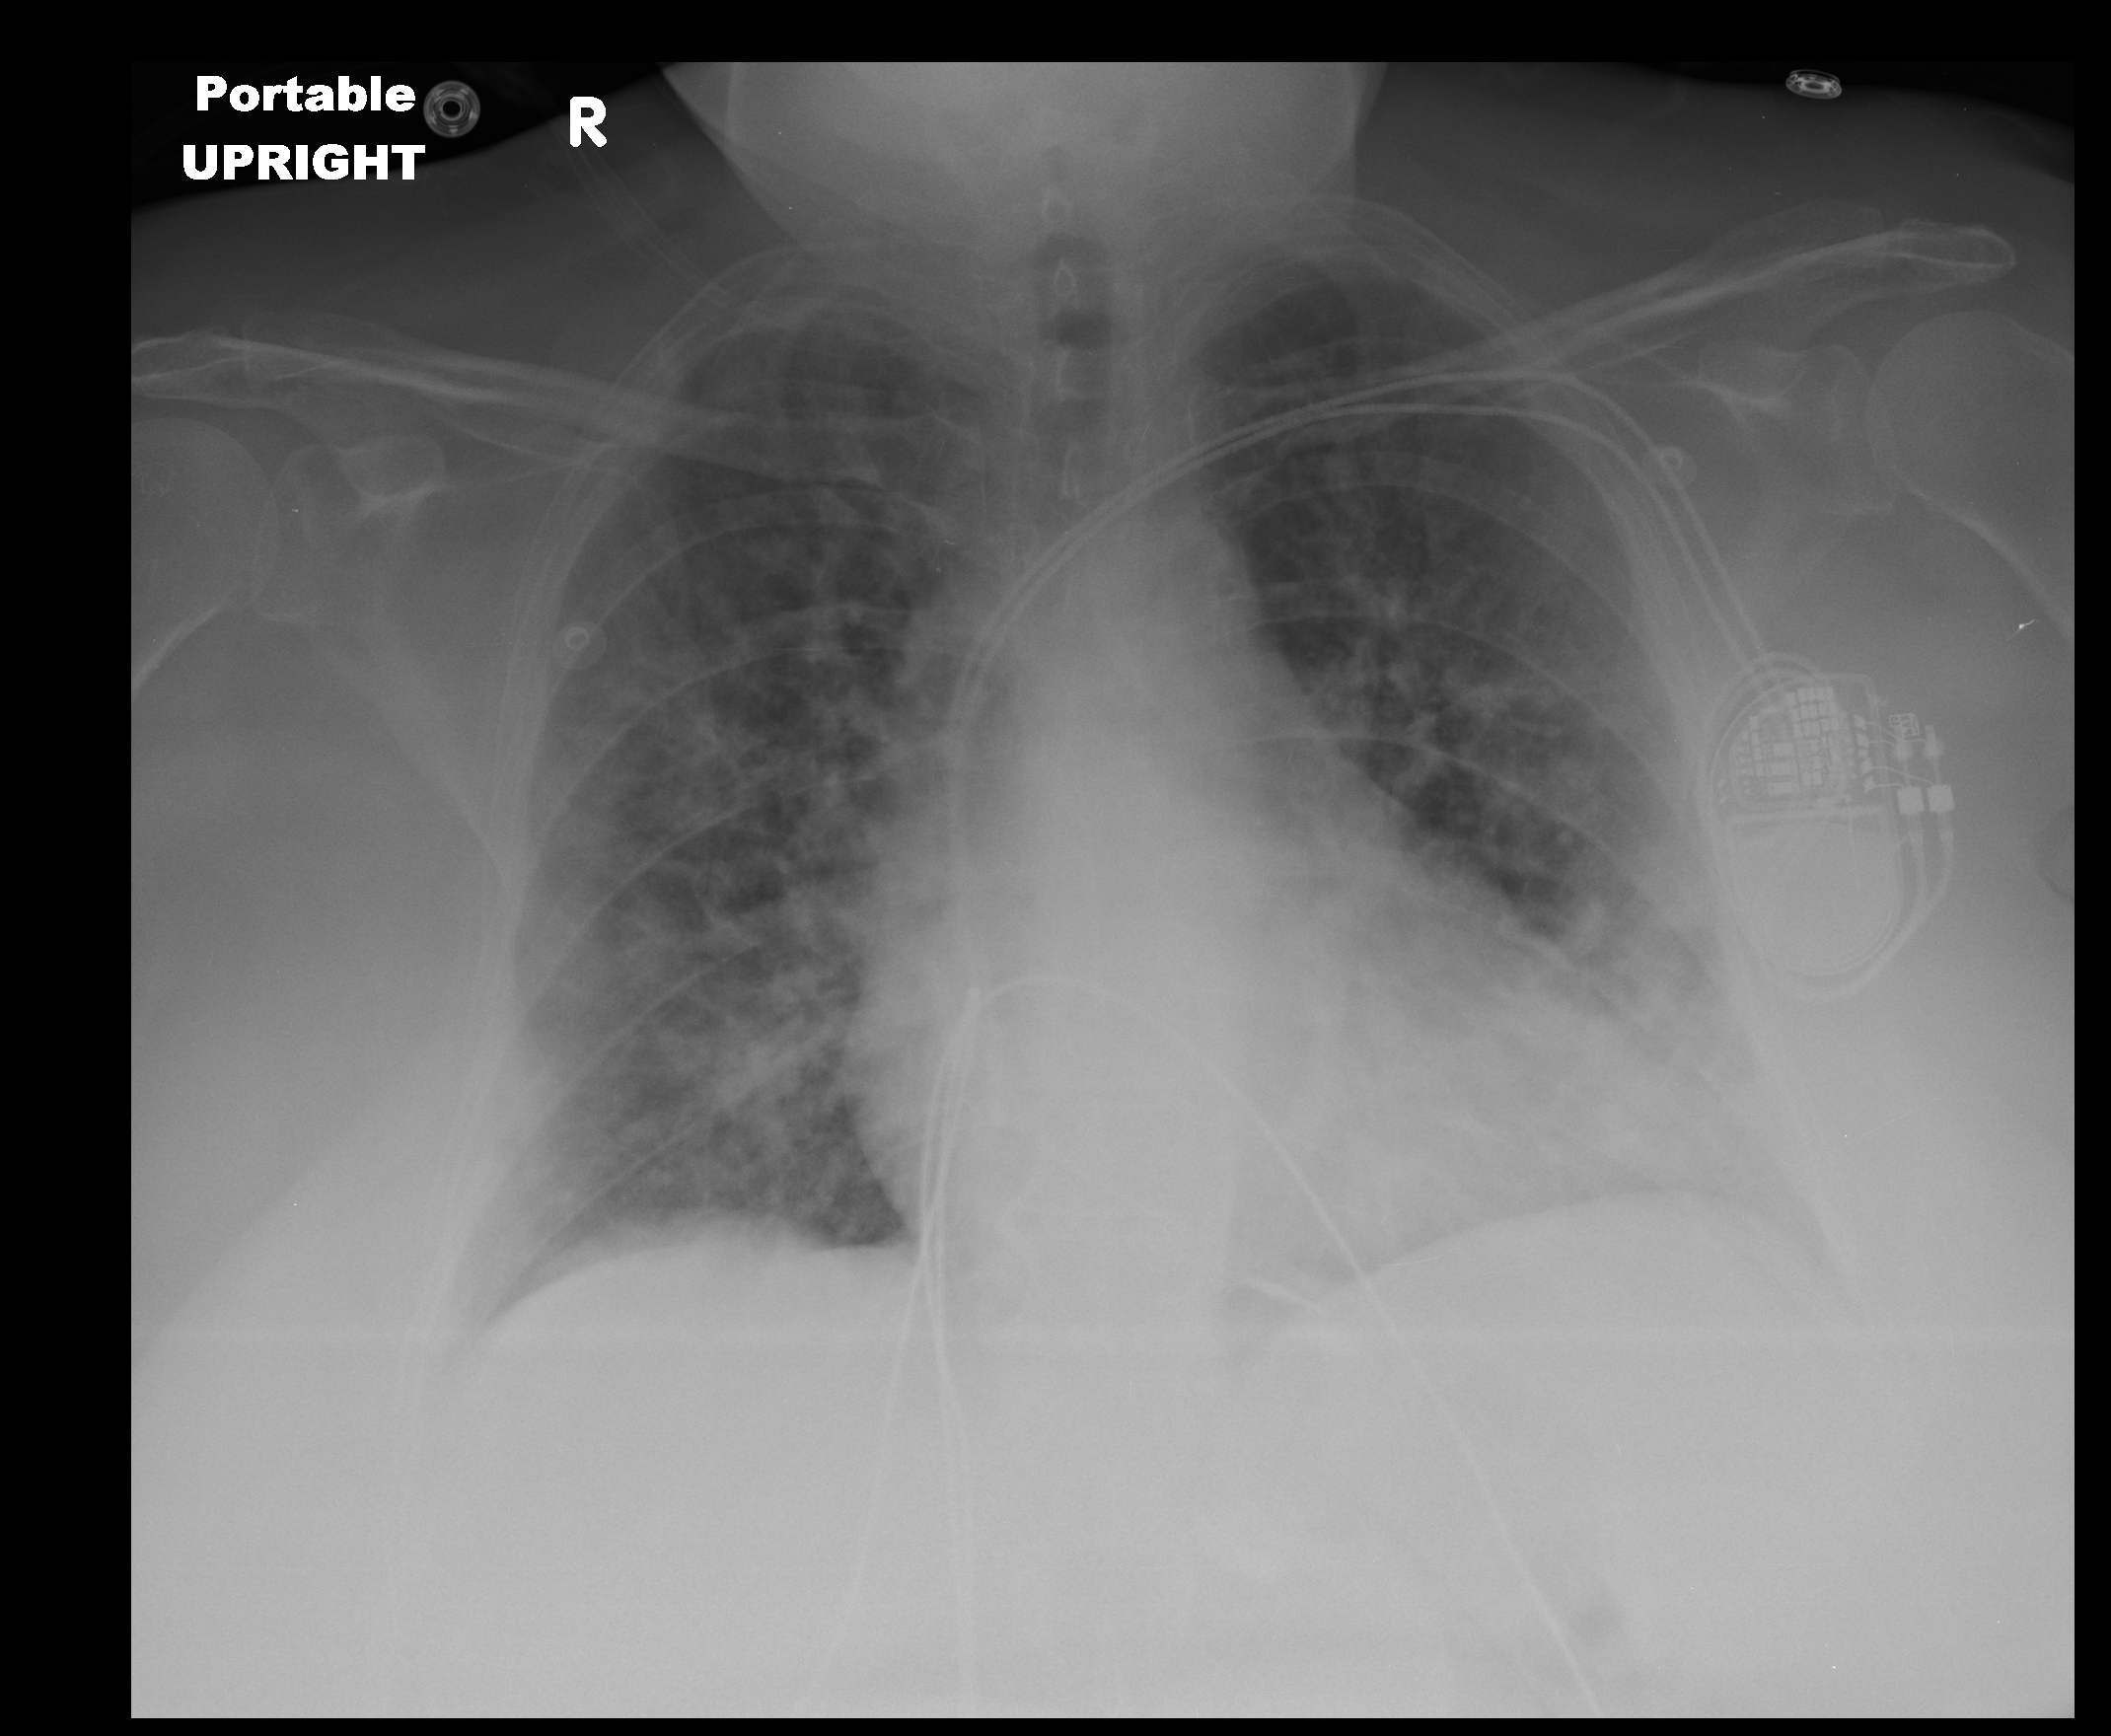
Portable chest radiograph, AP projection. Female patient, age 57 years; imaged 0 days after the COVID-19 diagnosis.
Radiologist key findings (as recorded): Worsening patchy, airspace opacities are seen throughout the bilateral lungs, predominantly within the lateral aspect of the left lower lung.